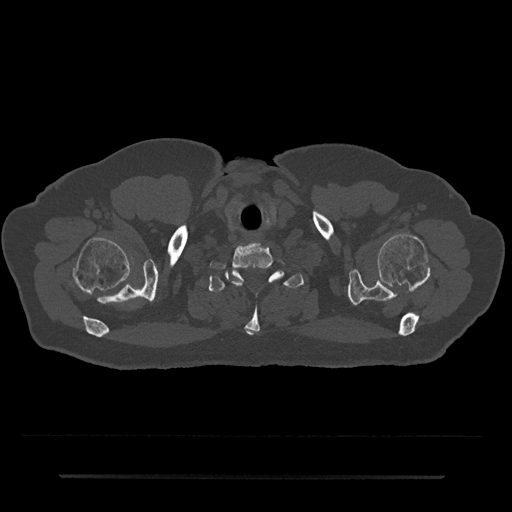
CT including the spine, one axial slice; slice 658 of 797 in the series (ordered by position); 120 kVp; bone window (W 1800 / L 400 HU); 0.5 mm slice thickness; 512 × 512 image matrix. Male patient, age 69 years. Case-level facts recorded for this patient, not image findings: primary cancer: prostate.
Annotated regions visible in this slice (semi-automatic segmentation, software-assisted and operator-edited):
- T1 vertebra: box from (x=208, y=271) to (x=304, y=335) px